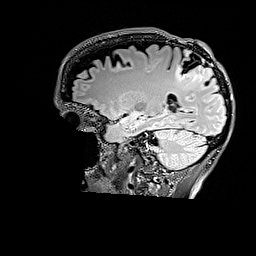
Brain MRI from a brain-tumour surgery series, one sagittal slice. T2 FLAIR. 1 mm slice thickness. 256 × 256 image matrix, field of view 256 × 256 mm. From the clinical record (not read from this slice): histopathology: Astrocytoma; WHO grade: 3; IDH mutation: yes; tumour location: Right Parietal.
Annotated regions visible in this slice (outlined manually by an expert reader):
- tumour: bounding box (x1, y1, x2, y2) in pixels: (175, 50, 214, 83)
- tumour: (190, 59, 214, 81)